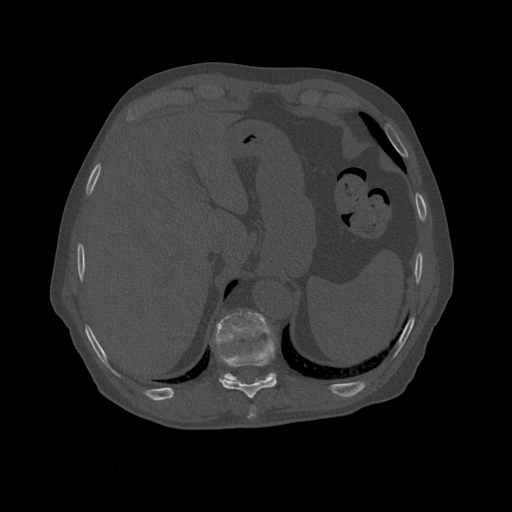
CT including the spine, one axial slice; slice 418 of 450 in the series (ordered by position); reconstruction kernel STANDARD; bone window (W 1800 / L 400 HU); 1.25 mm slice thickness; 512 × 512 image matrix, field of view 405 × 405 mm. Patient age 75 years. Case-level facts recorded for this patient, not image findings: primary cancer: prostate.
Outlined on this slice (semi-automatically segmented with operator editing):
- T10 vertebra: box from (x=214, y=310) to (x=275, y=381) px
- T8 vertebra: (x=251, y=406)–(x=257, y=411)
- T9 vertebra: (x=218, y=313)–(x=277, y=399)